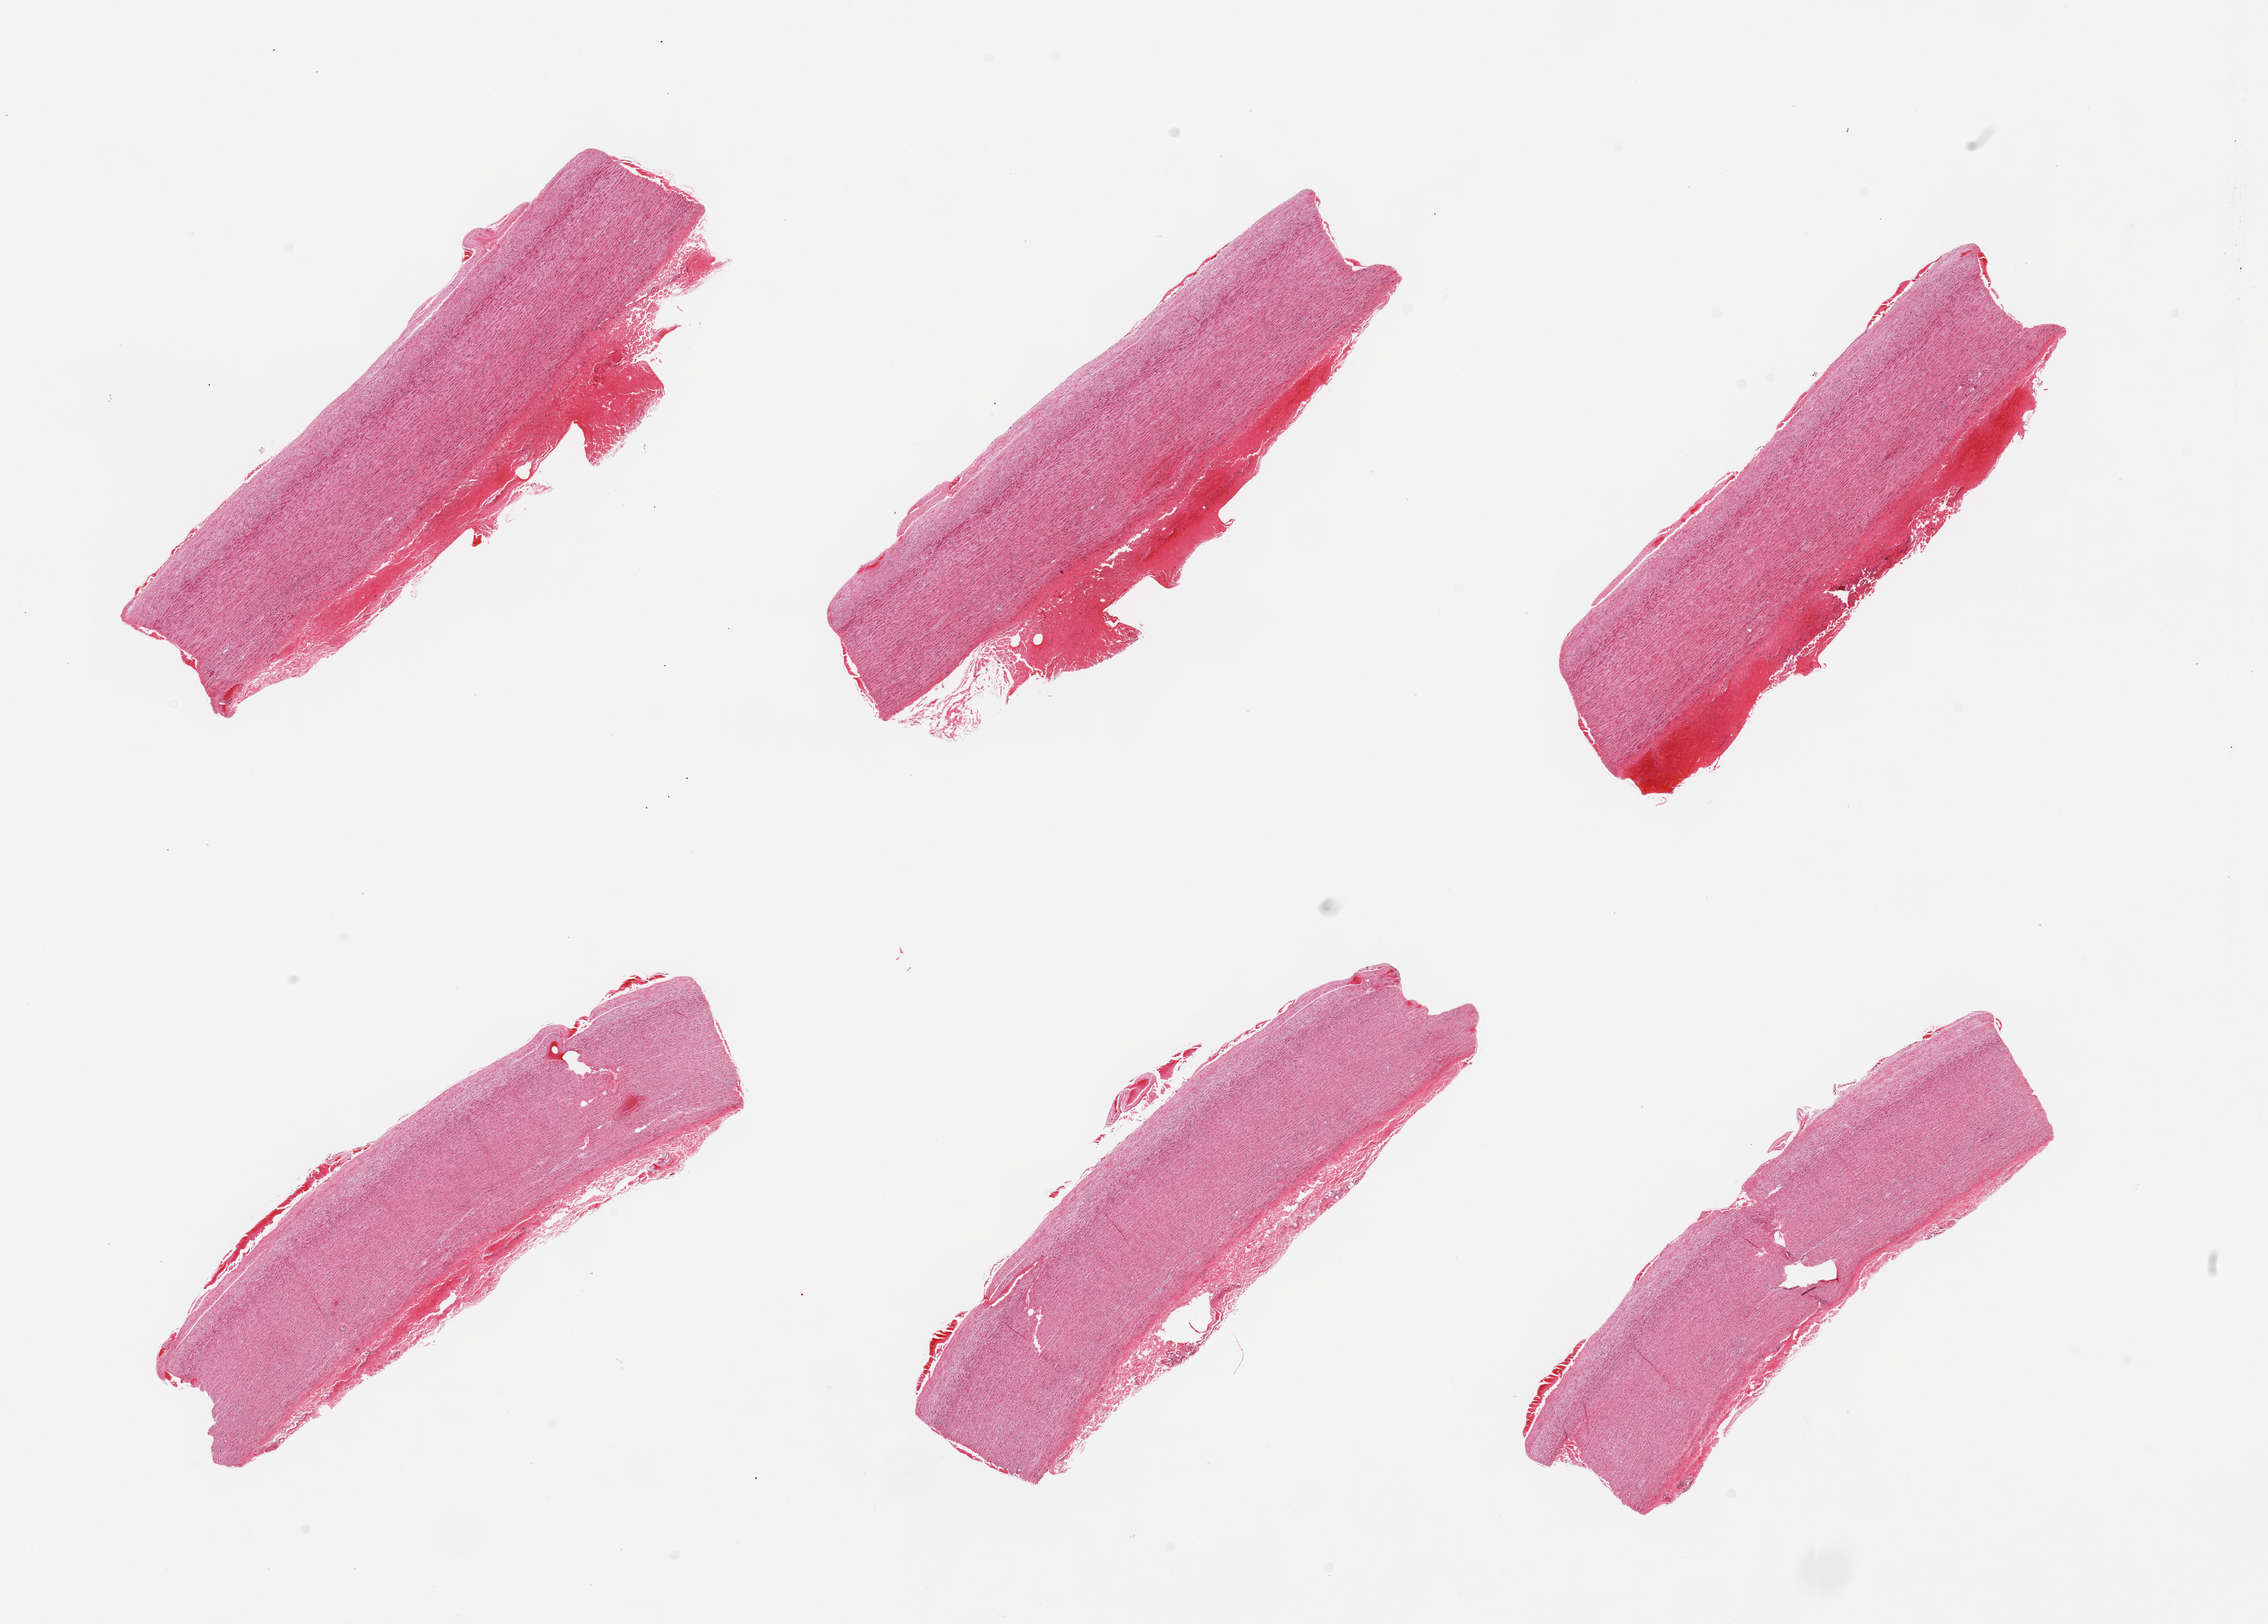
Digitized H&E-stained section, brightfield, shown as a low-resolution overview of the whole scanned area (about 24.6 x 17.6 mm, acquisition: 20x scan); PAXgene-fixed, paraffin-embedded tissue; target tissue: aorta; tissue donor sample. Donor: female.
• review note (as recorded): 6 pieces, atherosis up to ~0.4mm thicki